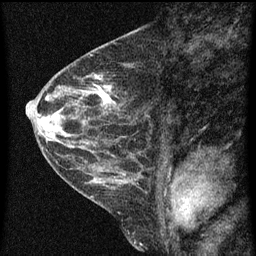
Breast MRI (dynamic contrast-enhanced), one sagittal slice; position 26 of 60 along the scan axis; dynamic contrast-enhanced series, image 2 of 3 at this slice position (ordered by acquisition); 1.5 T; TE 4.2 ms, TR 8 ms; 2 mm slice thickness; 256 × 256 image matrix, field of view 180 × 180 mm. Patient: female, 48 years.
Outlined on this slice (semi-automatically segmented with operator editing):
- analysis volume of interest (the breast-tissue region the enhancement analysis was run in; not a lesion): bounding box <82,72,122,125> (left, top, right, bottom; pixels)
- tumour enhancement mask (voxels above the 70 % enhancement threshold inside the analysis volume of interest): <95,86,116,105>